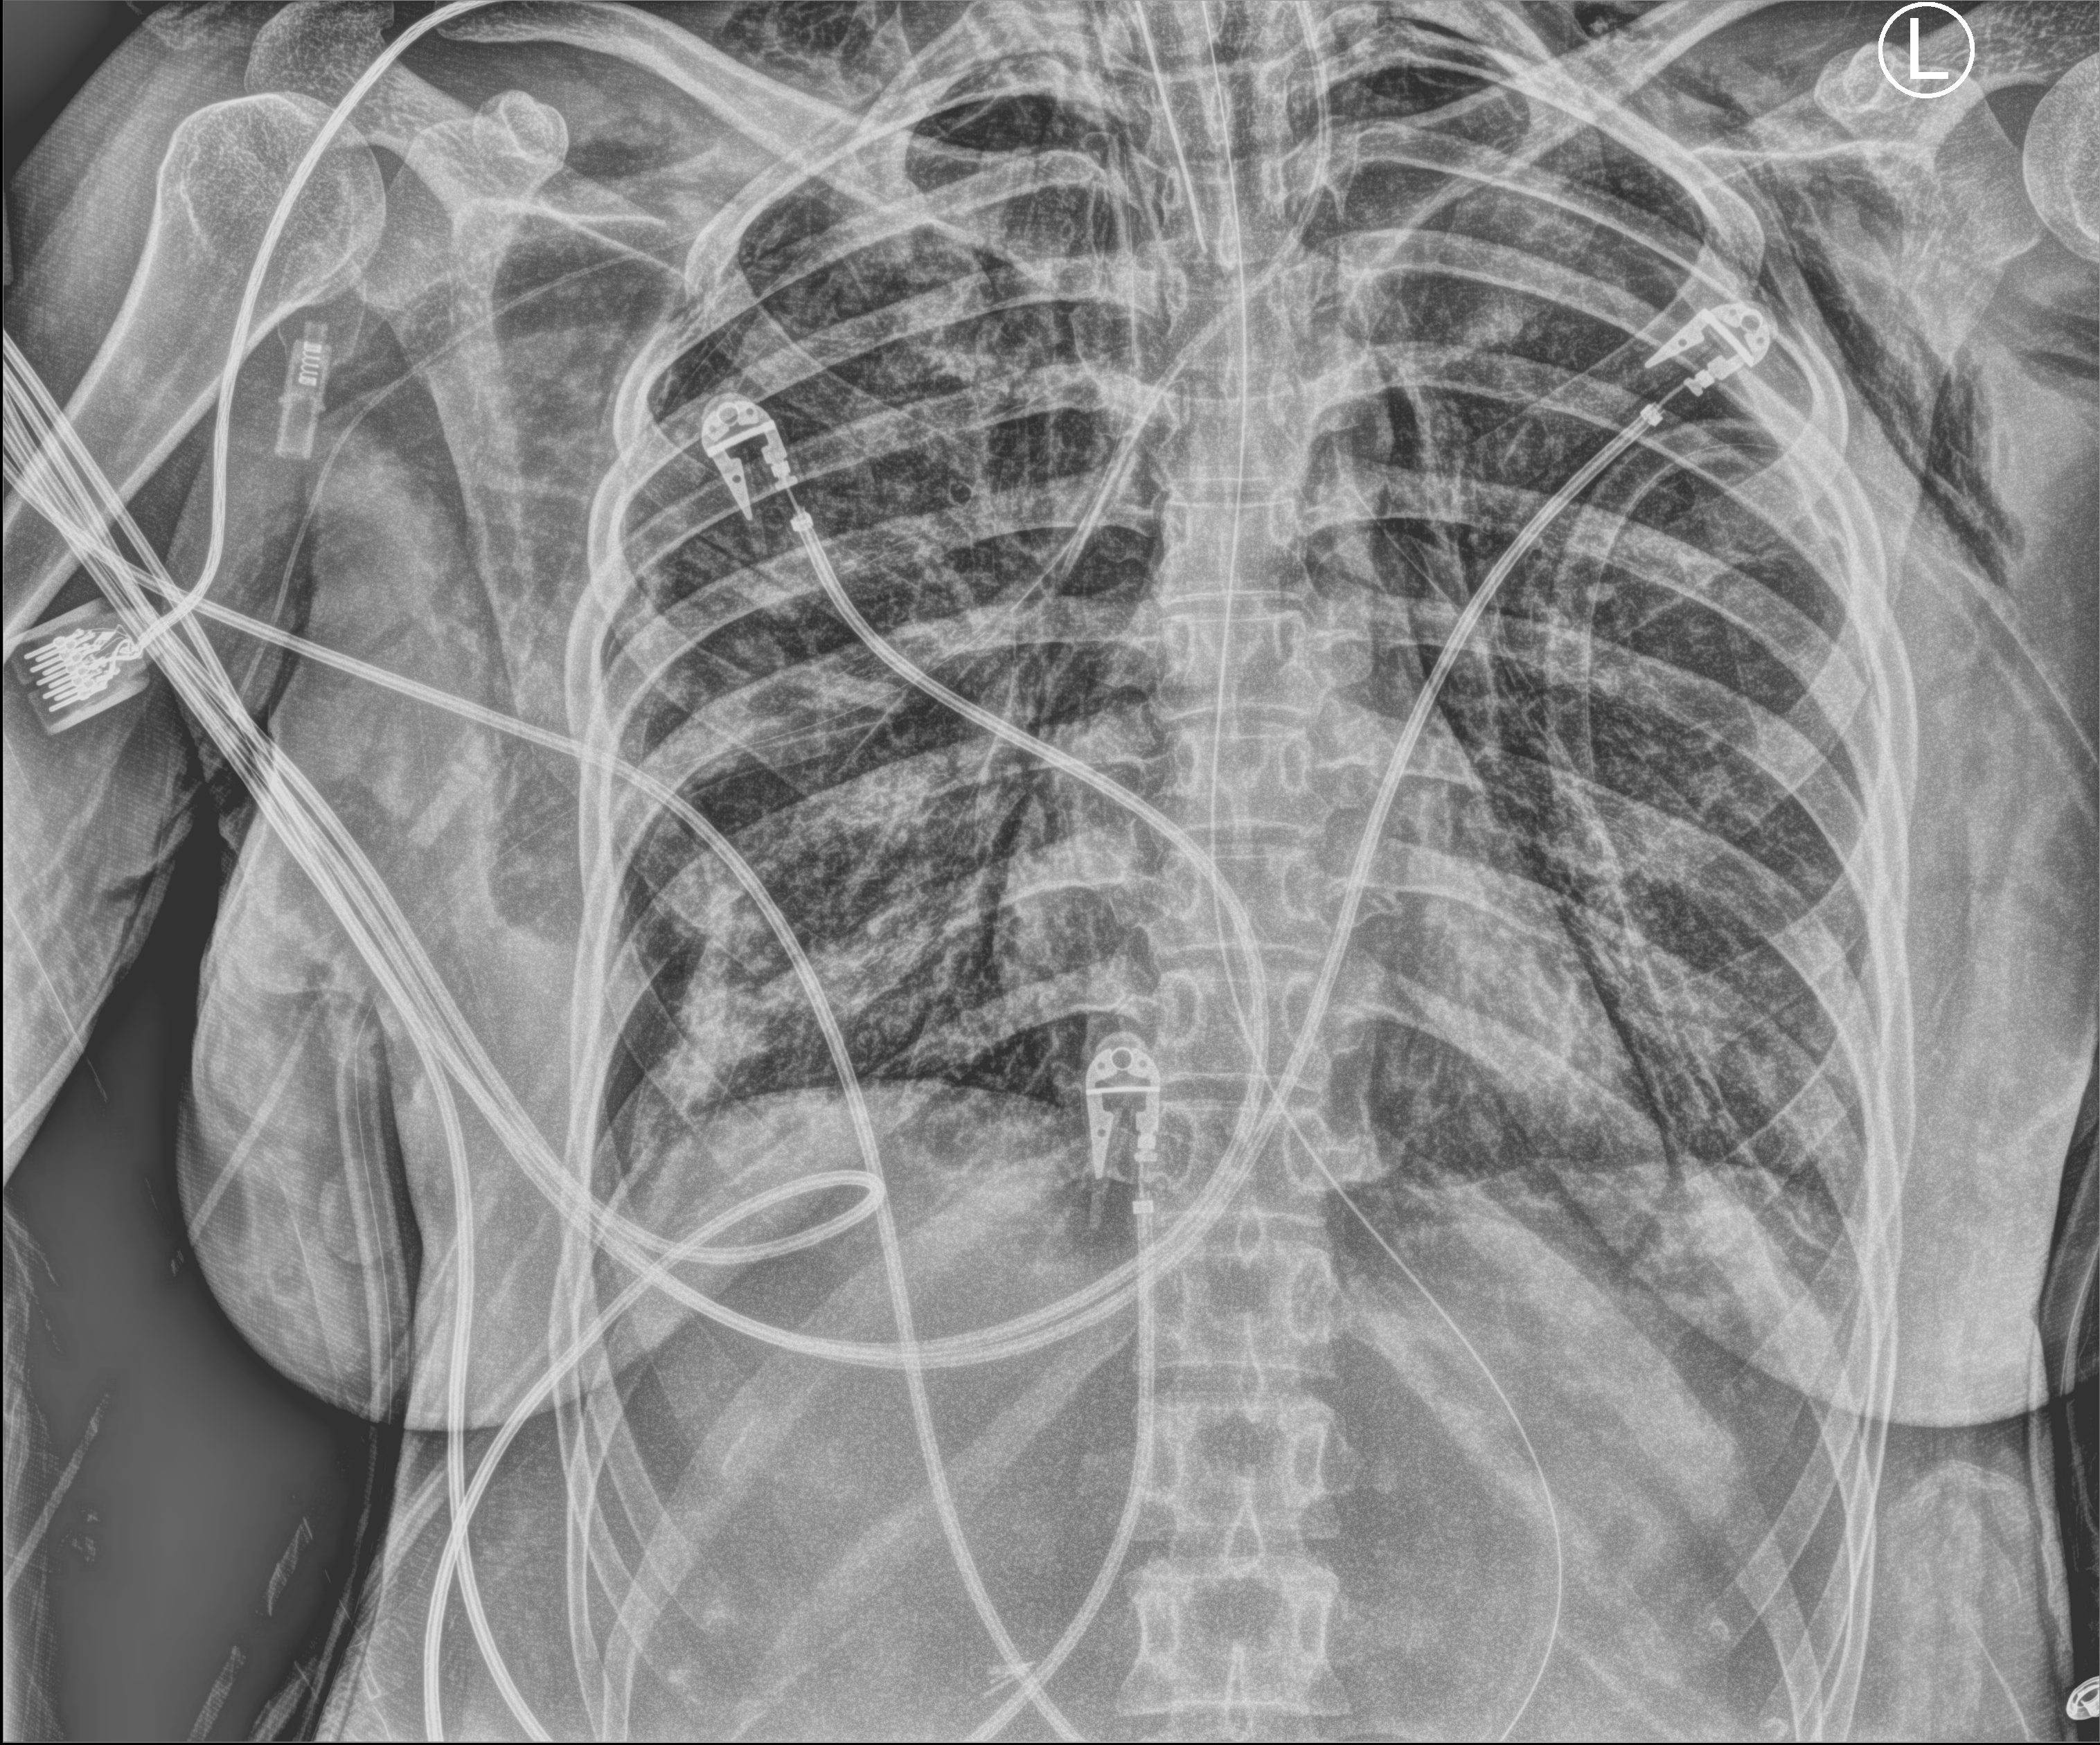
Portable chest radiograph; anteroposterior (AP) projection. Adult patient hospitalised with COVID-19, age 18–59 years.
From the hospital-stay record, not from the radiograph (when in the stay this image was taken is not recorded): mechanically ventilated during this hospital stay: yes.